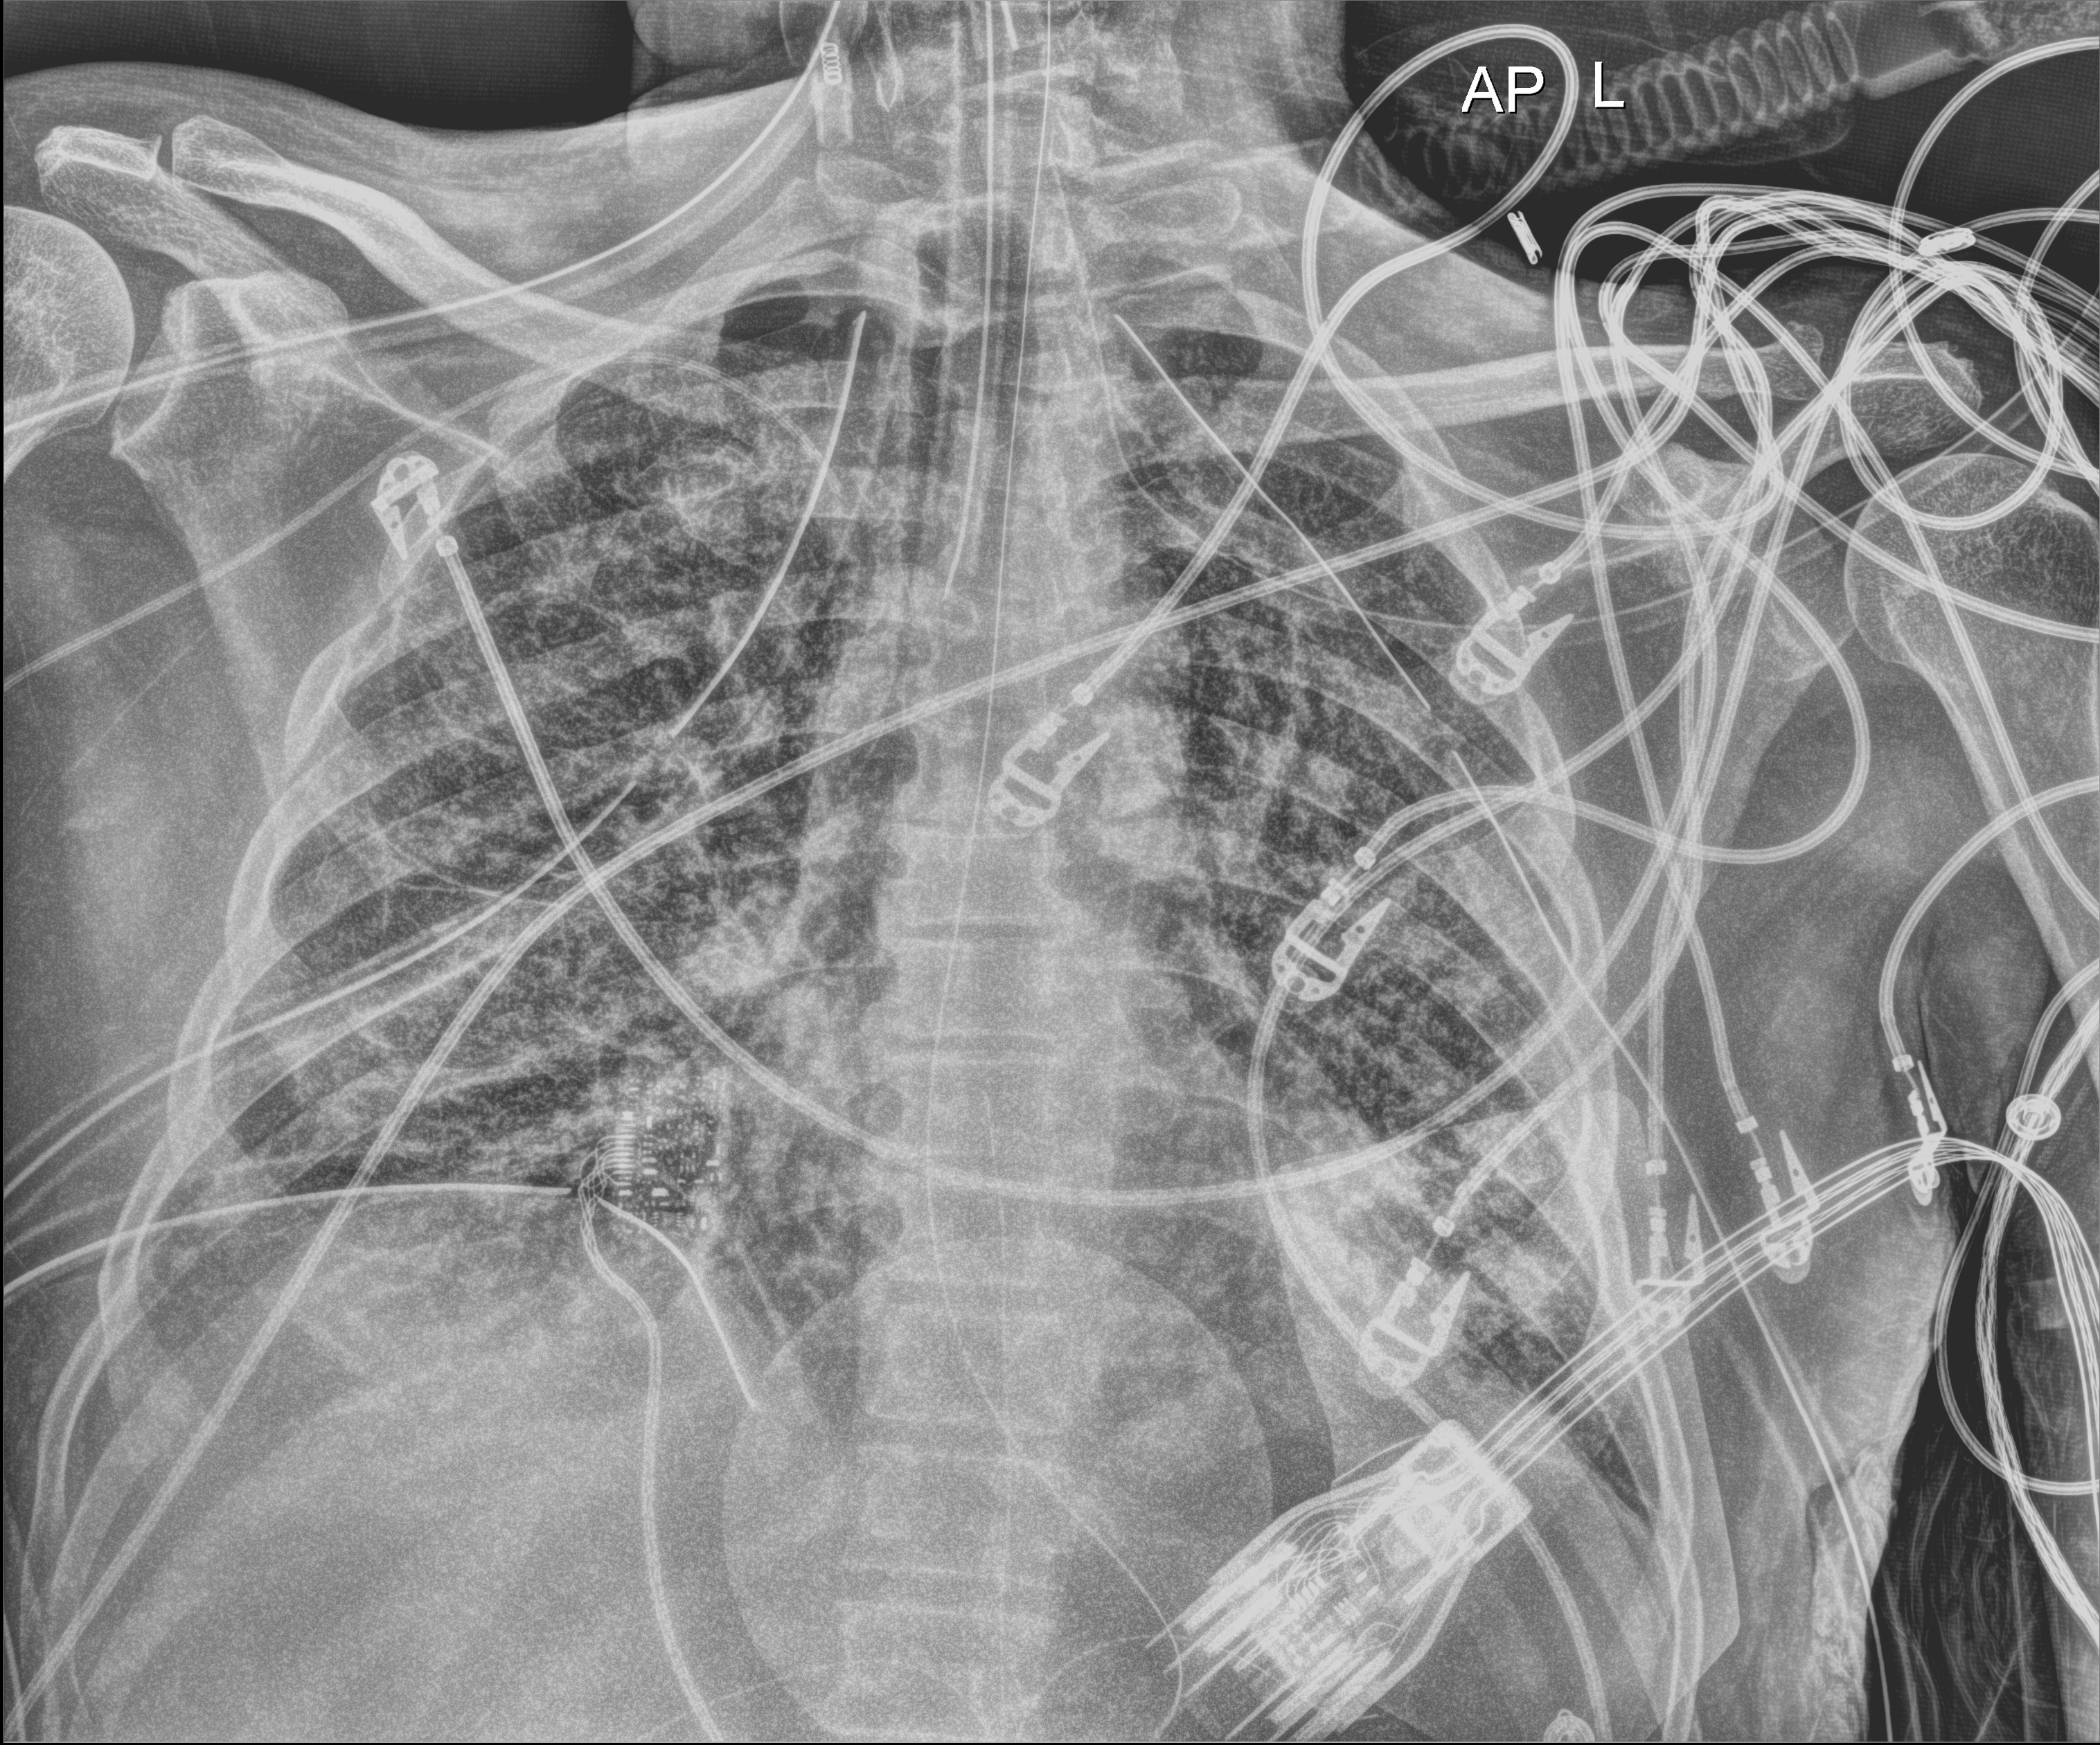
Chest X-ray (portable), anteroposterior (AP) projection. Patient hospitalised with COVID-19; male, aged 18–59 years.
From the hospital-stay record, not from the radiograph (when in the stay this image was taken is not recorded): COPD (admission record): no; admitted to intensive care during this hospital stay: yes.